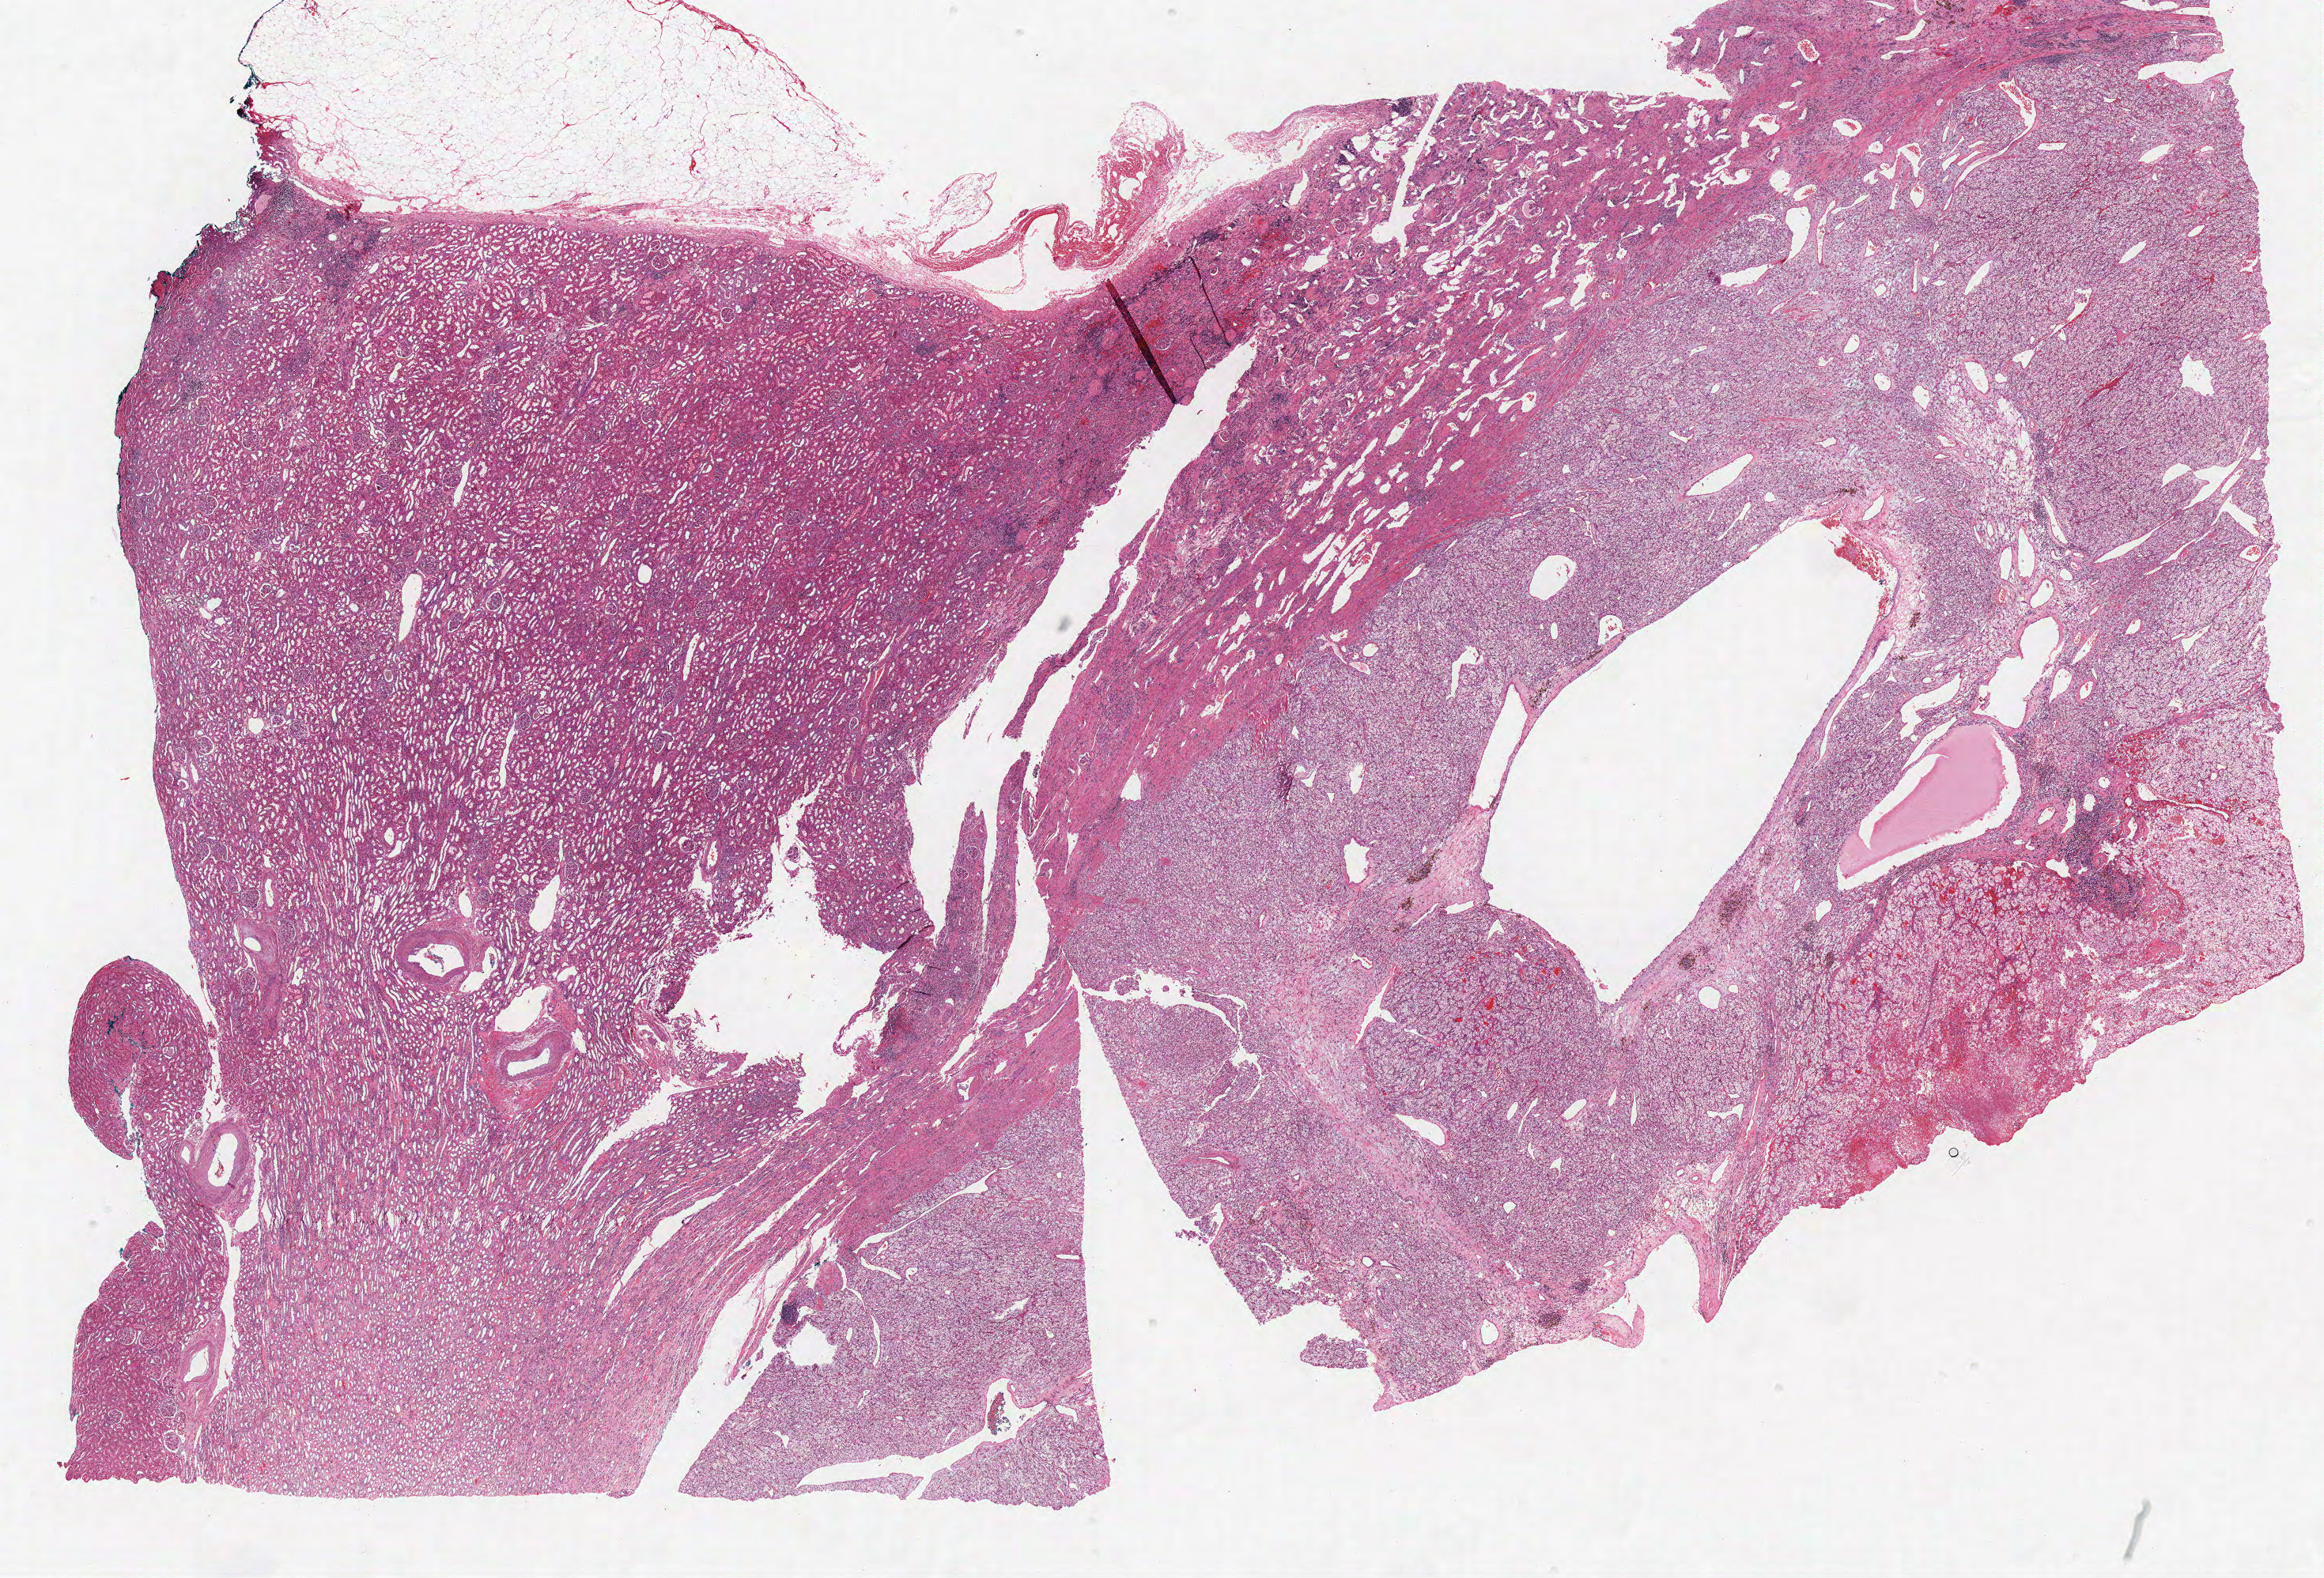
Whole-slide histology image, H&E-stained, whole scanned area (about 23.5 x 16.0 mm, slide scanned at 40x) shown as a low-resolution overview; formalin-fixed paraffin-embedded (FFPE) diagnostic section; sample: primary tumour, kidney. Patient: male, age at initial diagnosis 79 years. Histologic grade: G3 (poorly differentiated).
* TNM: T3a NX M0
* histologic diagnosis: Clear cell adenocarcinoma, NOS
* AJCC pathologic stage: III (6th edition)